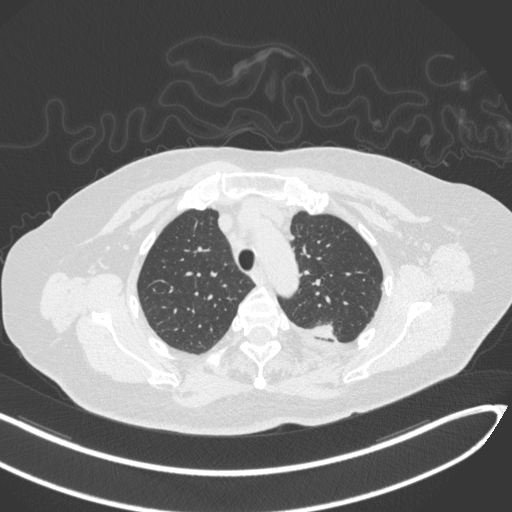
Chest CT, one axial slice; position 252 of 270 along the scan axis; 120 kVp; lung window (W 1500 / L -600 HU); 1 mm slice thickness; 512 × 512 image matrix, field of view 400 × 400 mm. Patient: female, 76 years. From the clinical record (not read from this slice): clinical TNM (as recorded): T1c N0 M0.
Structures marked on this image (rectangle marked by the reading radiologist):
- lung tumour (recorded histology: adenocarcinoma): bounding box <312,319,340,346> (left, top, right, bottom; pixels)